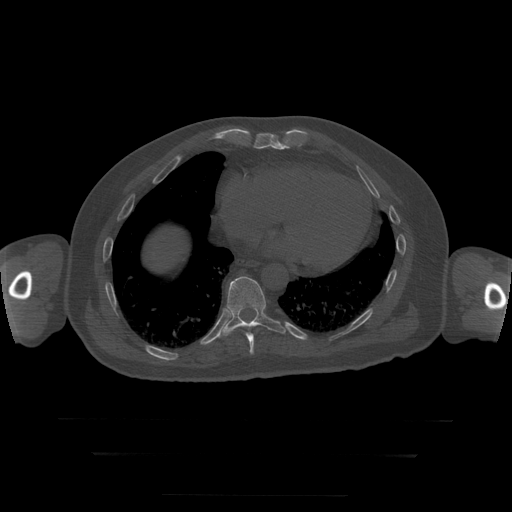
CT including the spine, one axial slice; slice 129 of 397 in the series (ordered by position); reconstruction kernel STANDARD; 120 kVp; bone window (W 1800 / L 400 HU); 1.25 mm slice thickness; 512 × 512 image matrix, field of view 510 × 510 mm. Patient age 73 years. Case-level facts recorded for this patient, not image findings: primary cancer: prostate.
Structures marked on this image (semi-automatically segmented with operator editing):
- T10 vertebra: bounding box [x1, y1, x2, y2] px = [217, 277, 286, 338]
- T9 vertebra: [246, 333, 254, 355]